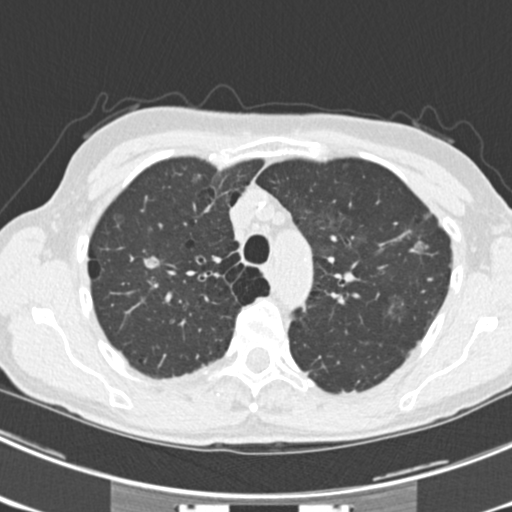
Low-dose screening chest CT, one axial slice; position 169 of 225 along the scan axis; reconstruction kernel B30f; lung window (W 1500 / L -600 HU); 512 × 512 image matrix, field of view 302 × 302 mm.
Outlined on this slice (outlined manually by an expert reader):
- lesion 3 (tumor, upper lobe of right lung): bounding box (x1, y1, x2, y2) in pixels: (144, 256, 160, 268)